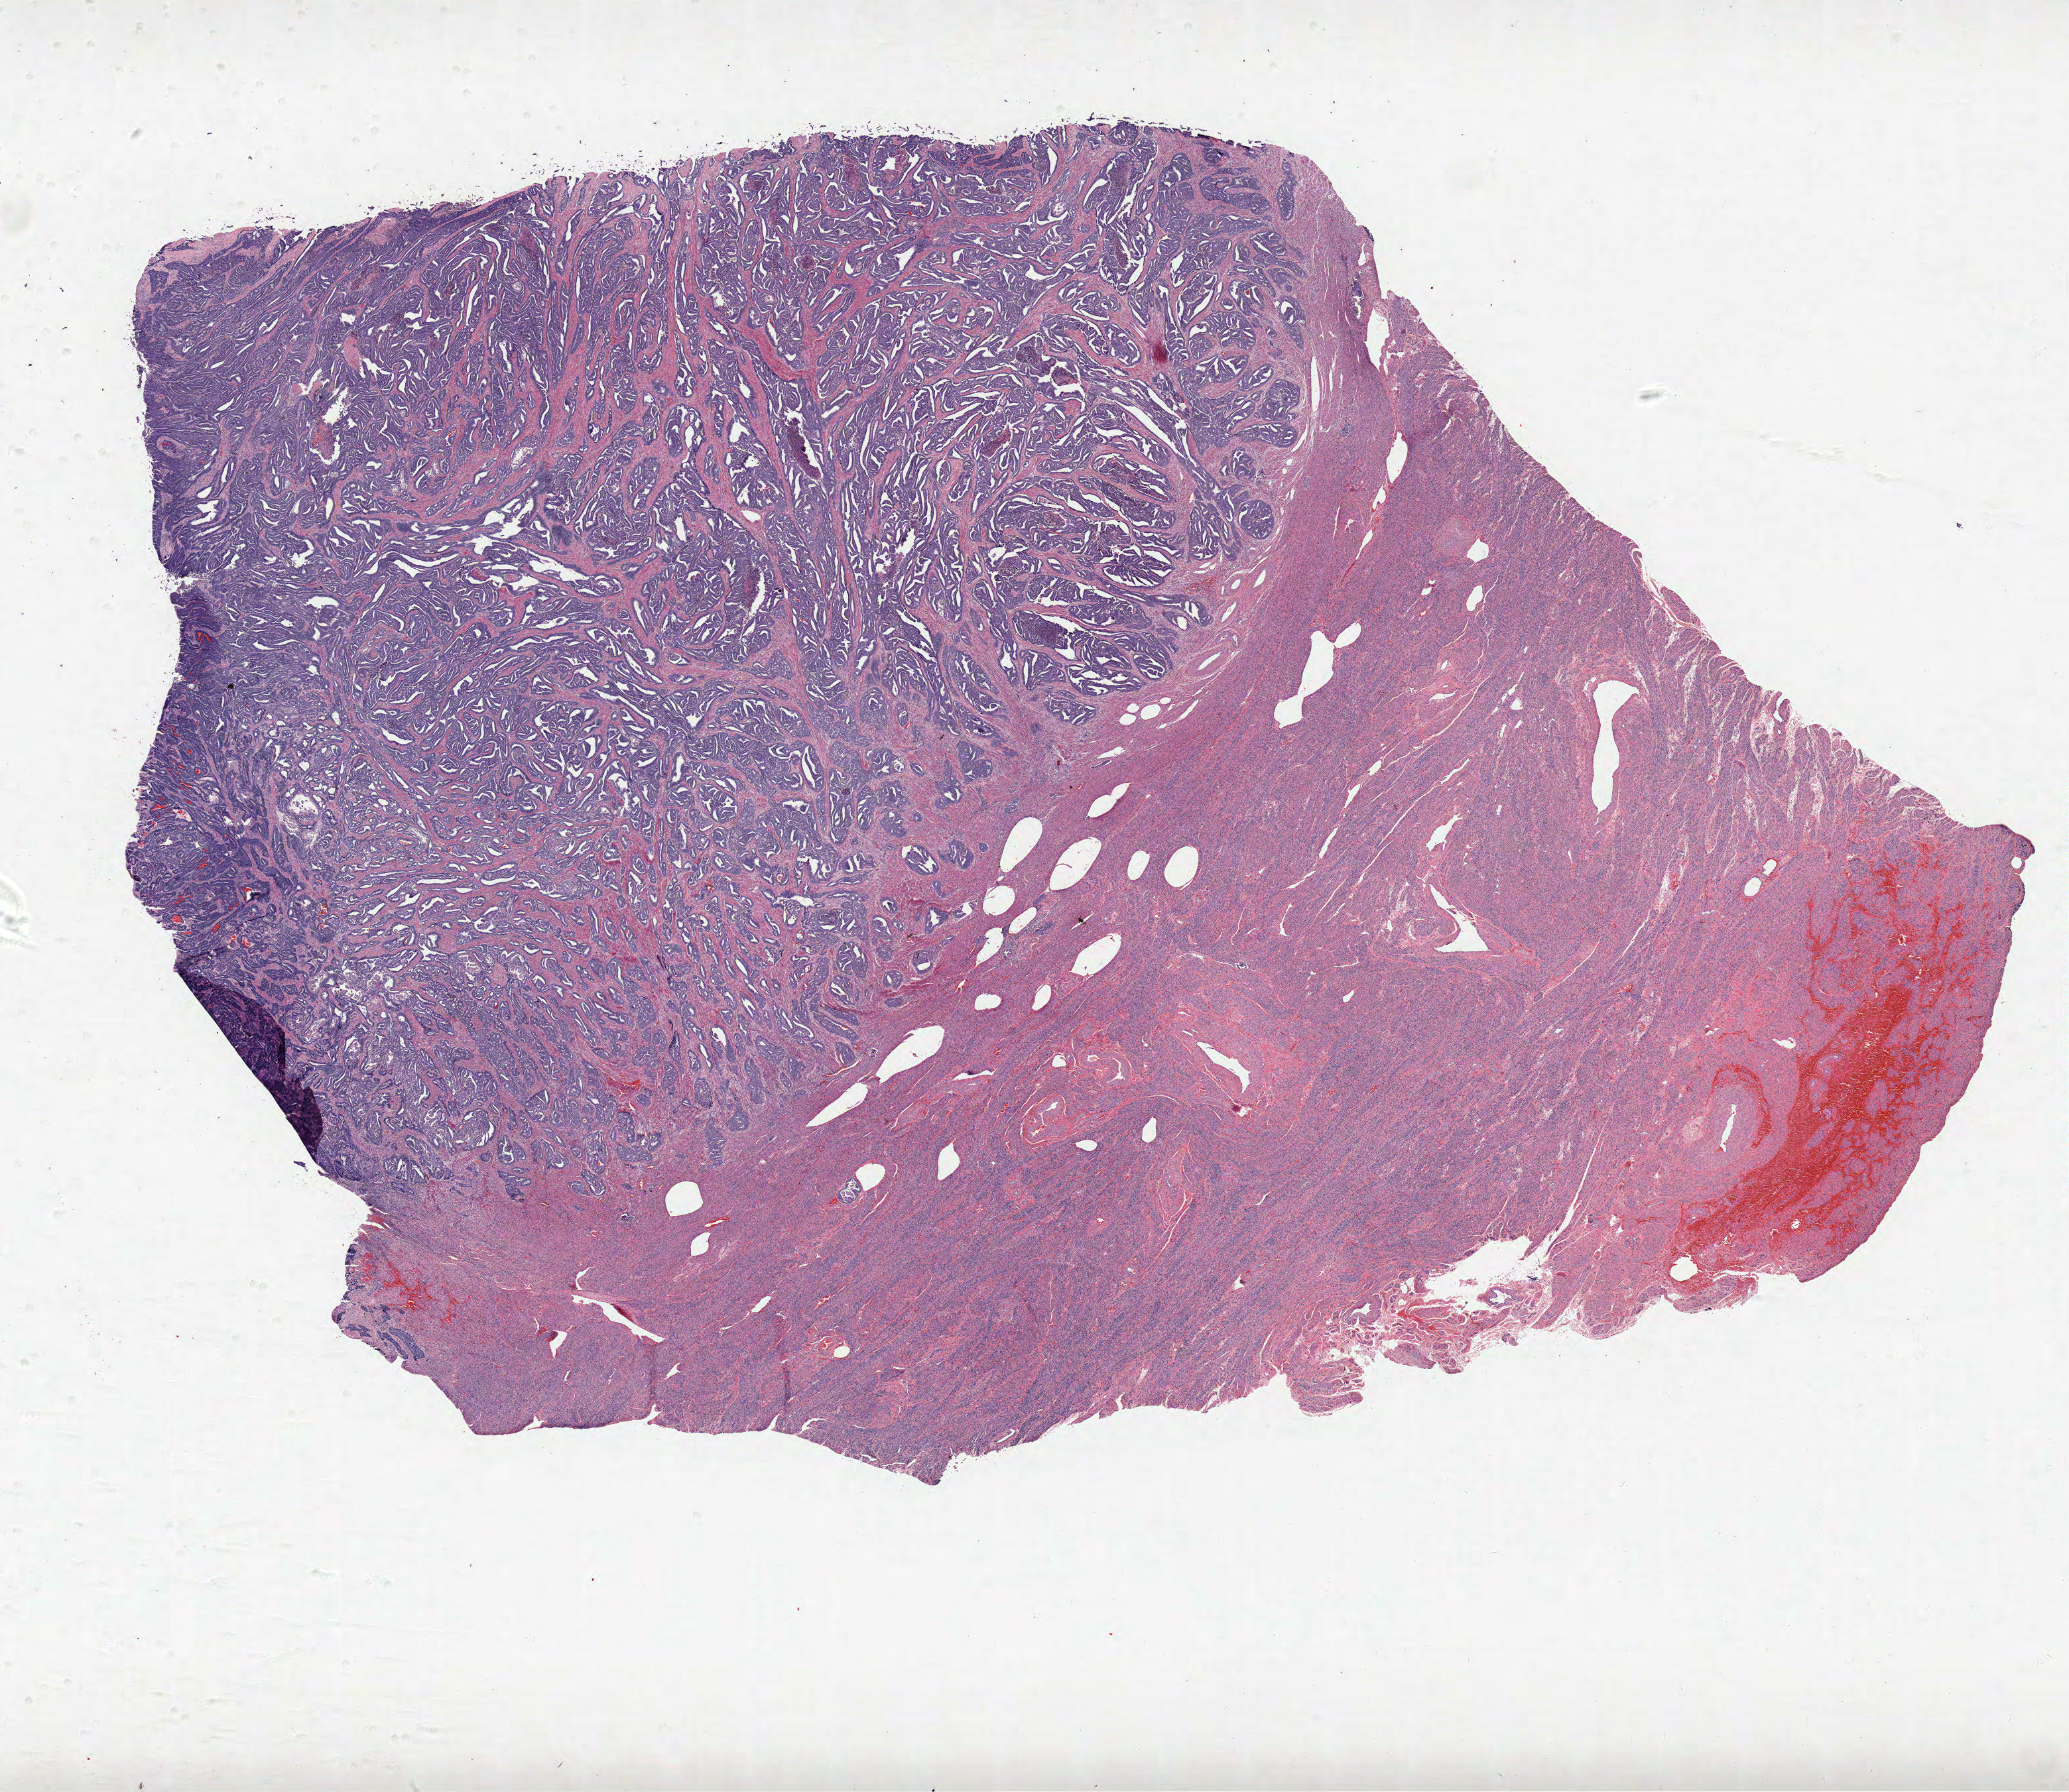
Whole-slide histology image, Hematoxylin and eosin (H&E) stained — whole scanned area (about 24.9 x 21.5 mm) shown as a low-resolution overview. Formalin-fixed paraffin-embedded (FFPE) diagnostic section. Uterus, primary tumour sample. Female patient; age at initial diagnosis 54 years.
Pathologic diagnosis: Endometrioid adenocarcinoma, NOS (endometrium).